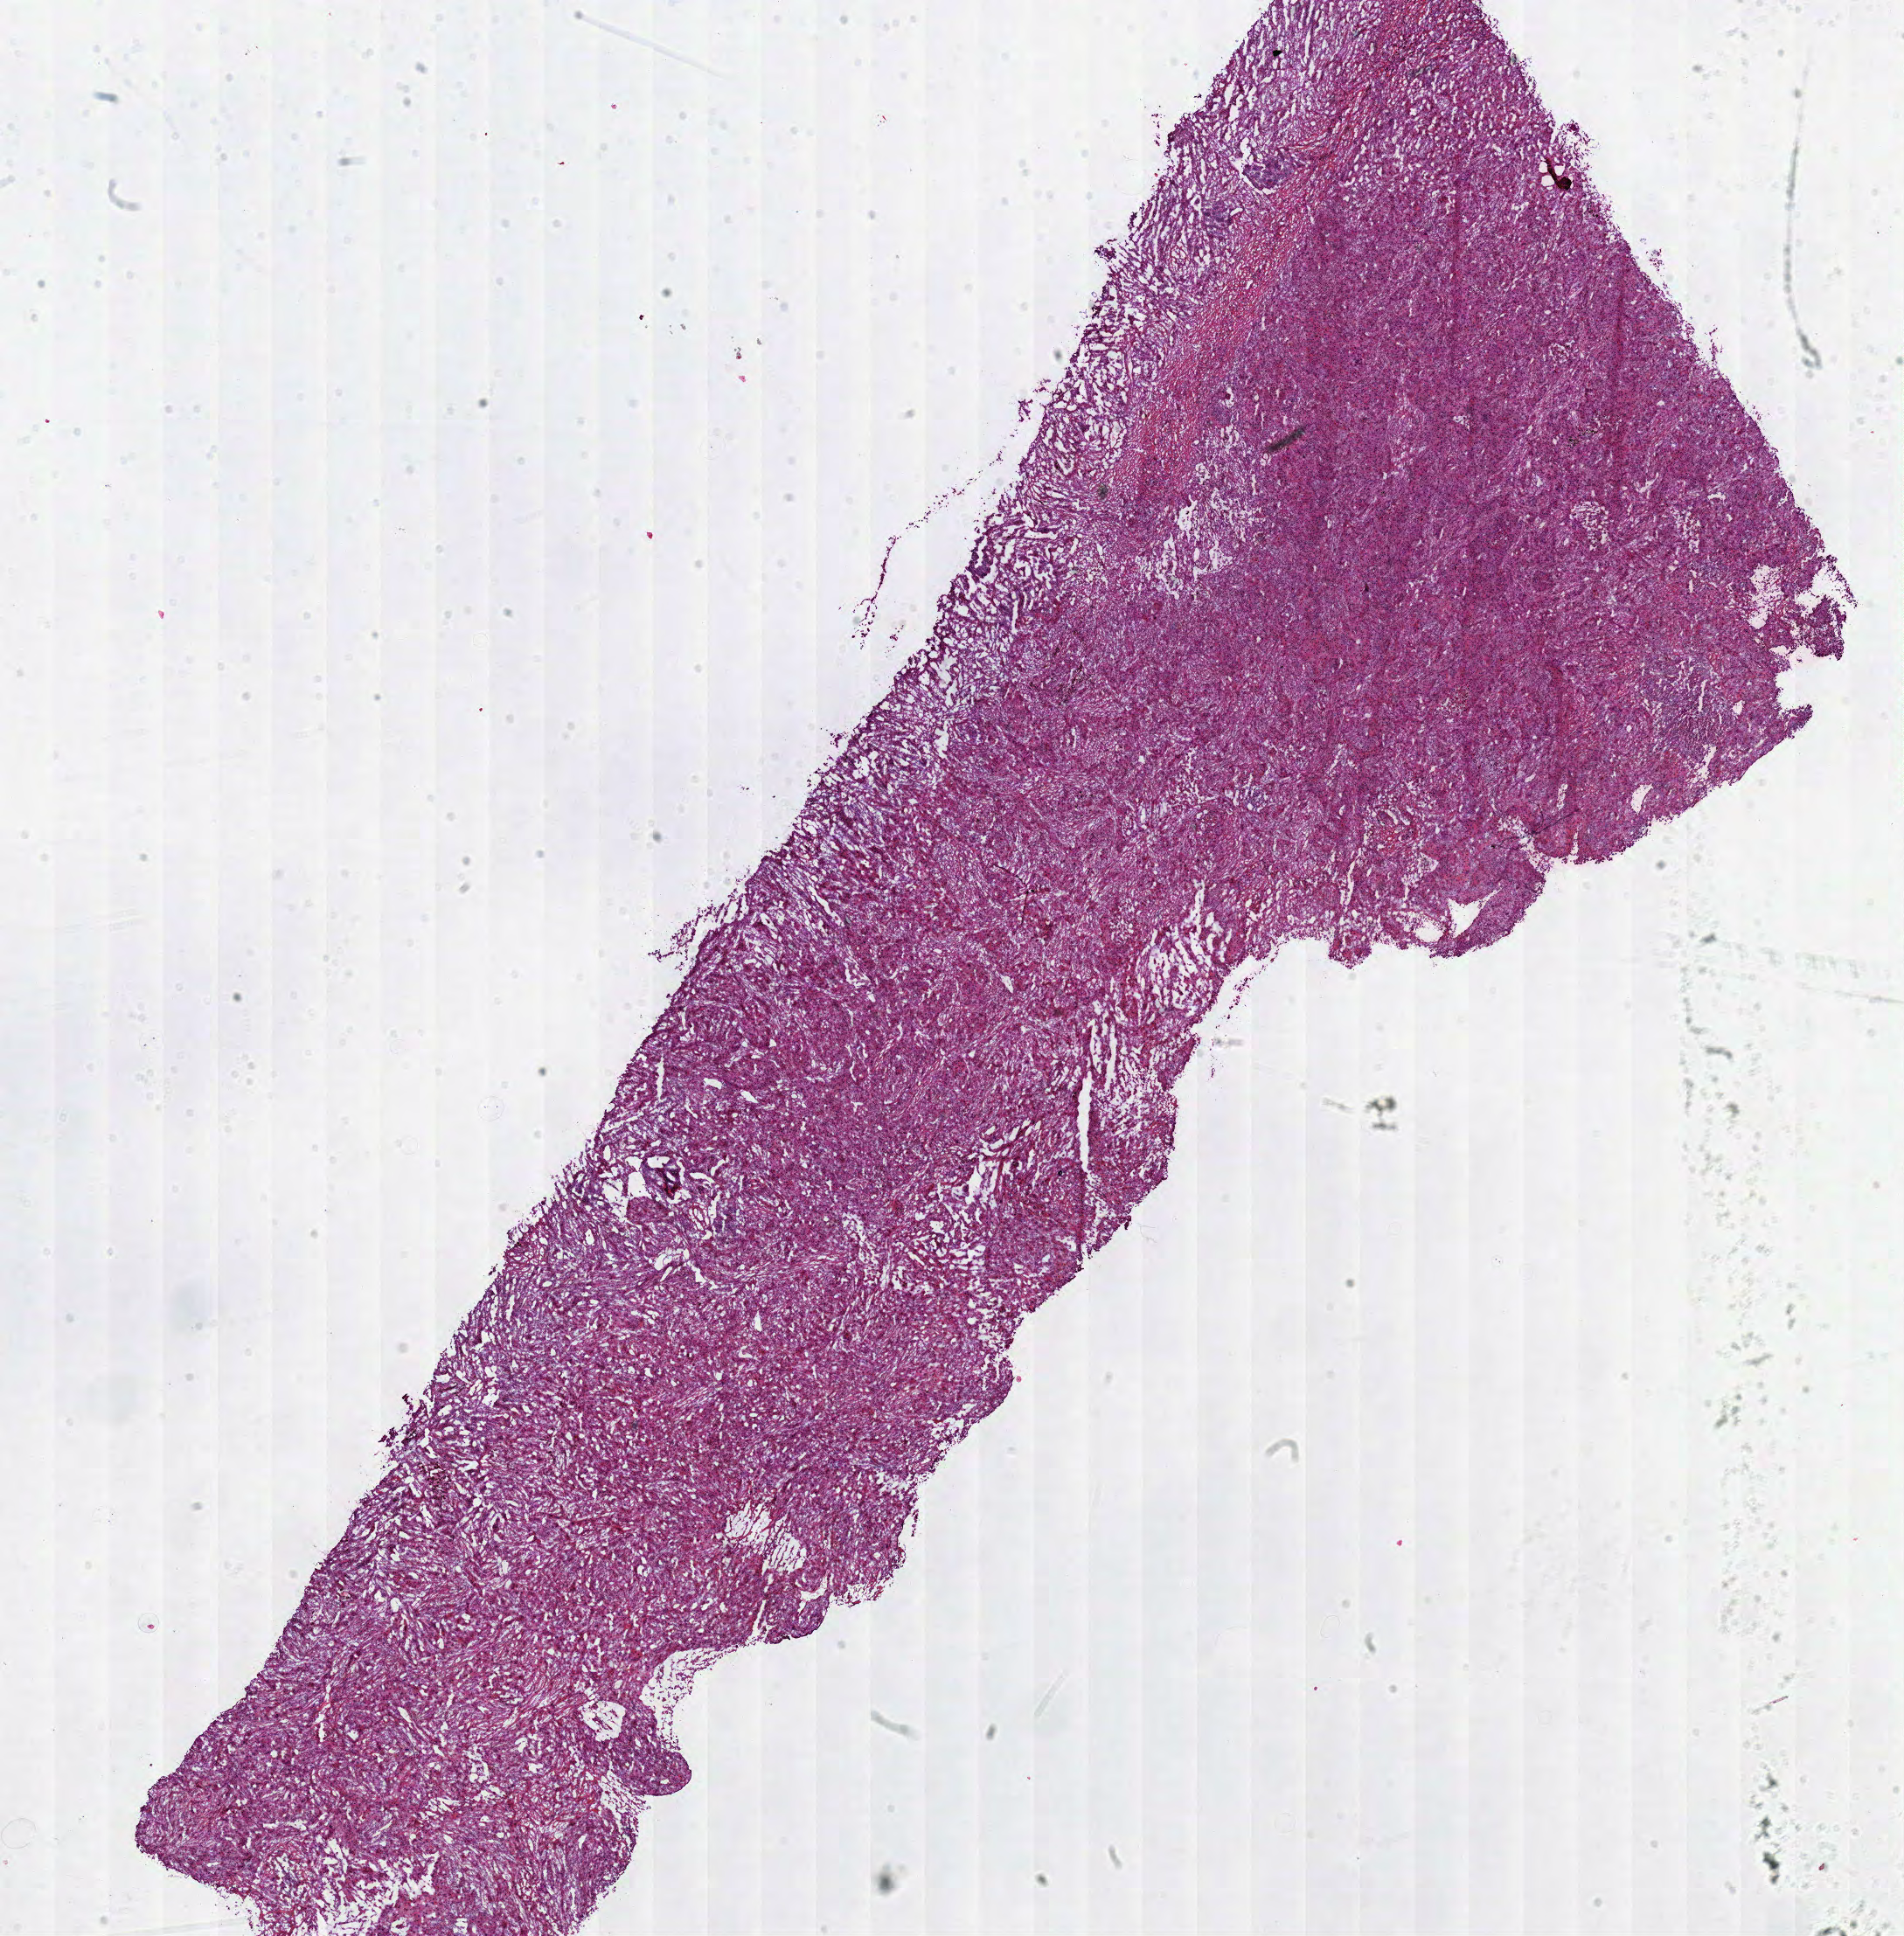
Whole-slide histology image, Hematoxylin and eosin (H&E) stained, whole scanned area (about 17.1 x 17.4 mm, acquisition: 40x scan) shown as a low-resolution overview; frozen section from the top of the tissue portion; lung, primary tumour sample. Patient: male, age at initial diagnosis 47 years. Composition of this section per pathologist review: tumour cells 67%, tumour nuclei 70%, normal cells 15%, stromal cells 10%, necrosis 8%.
Pathologic diagnosis: Squamous cell carcinoma, NOS (upper lobe, lung). Laterality: right. TNM: T3 N1 M0. AJCC pathologic stage: IIIA (6th edition).